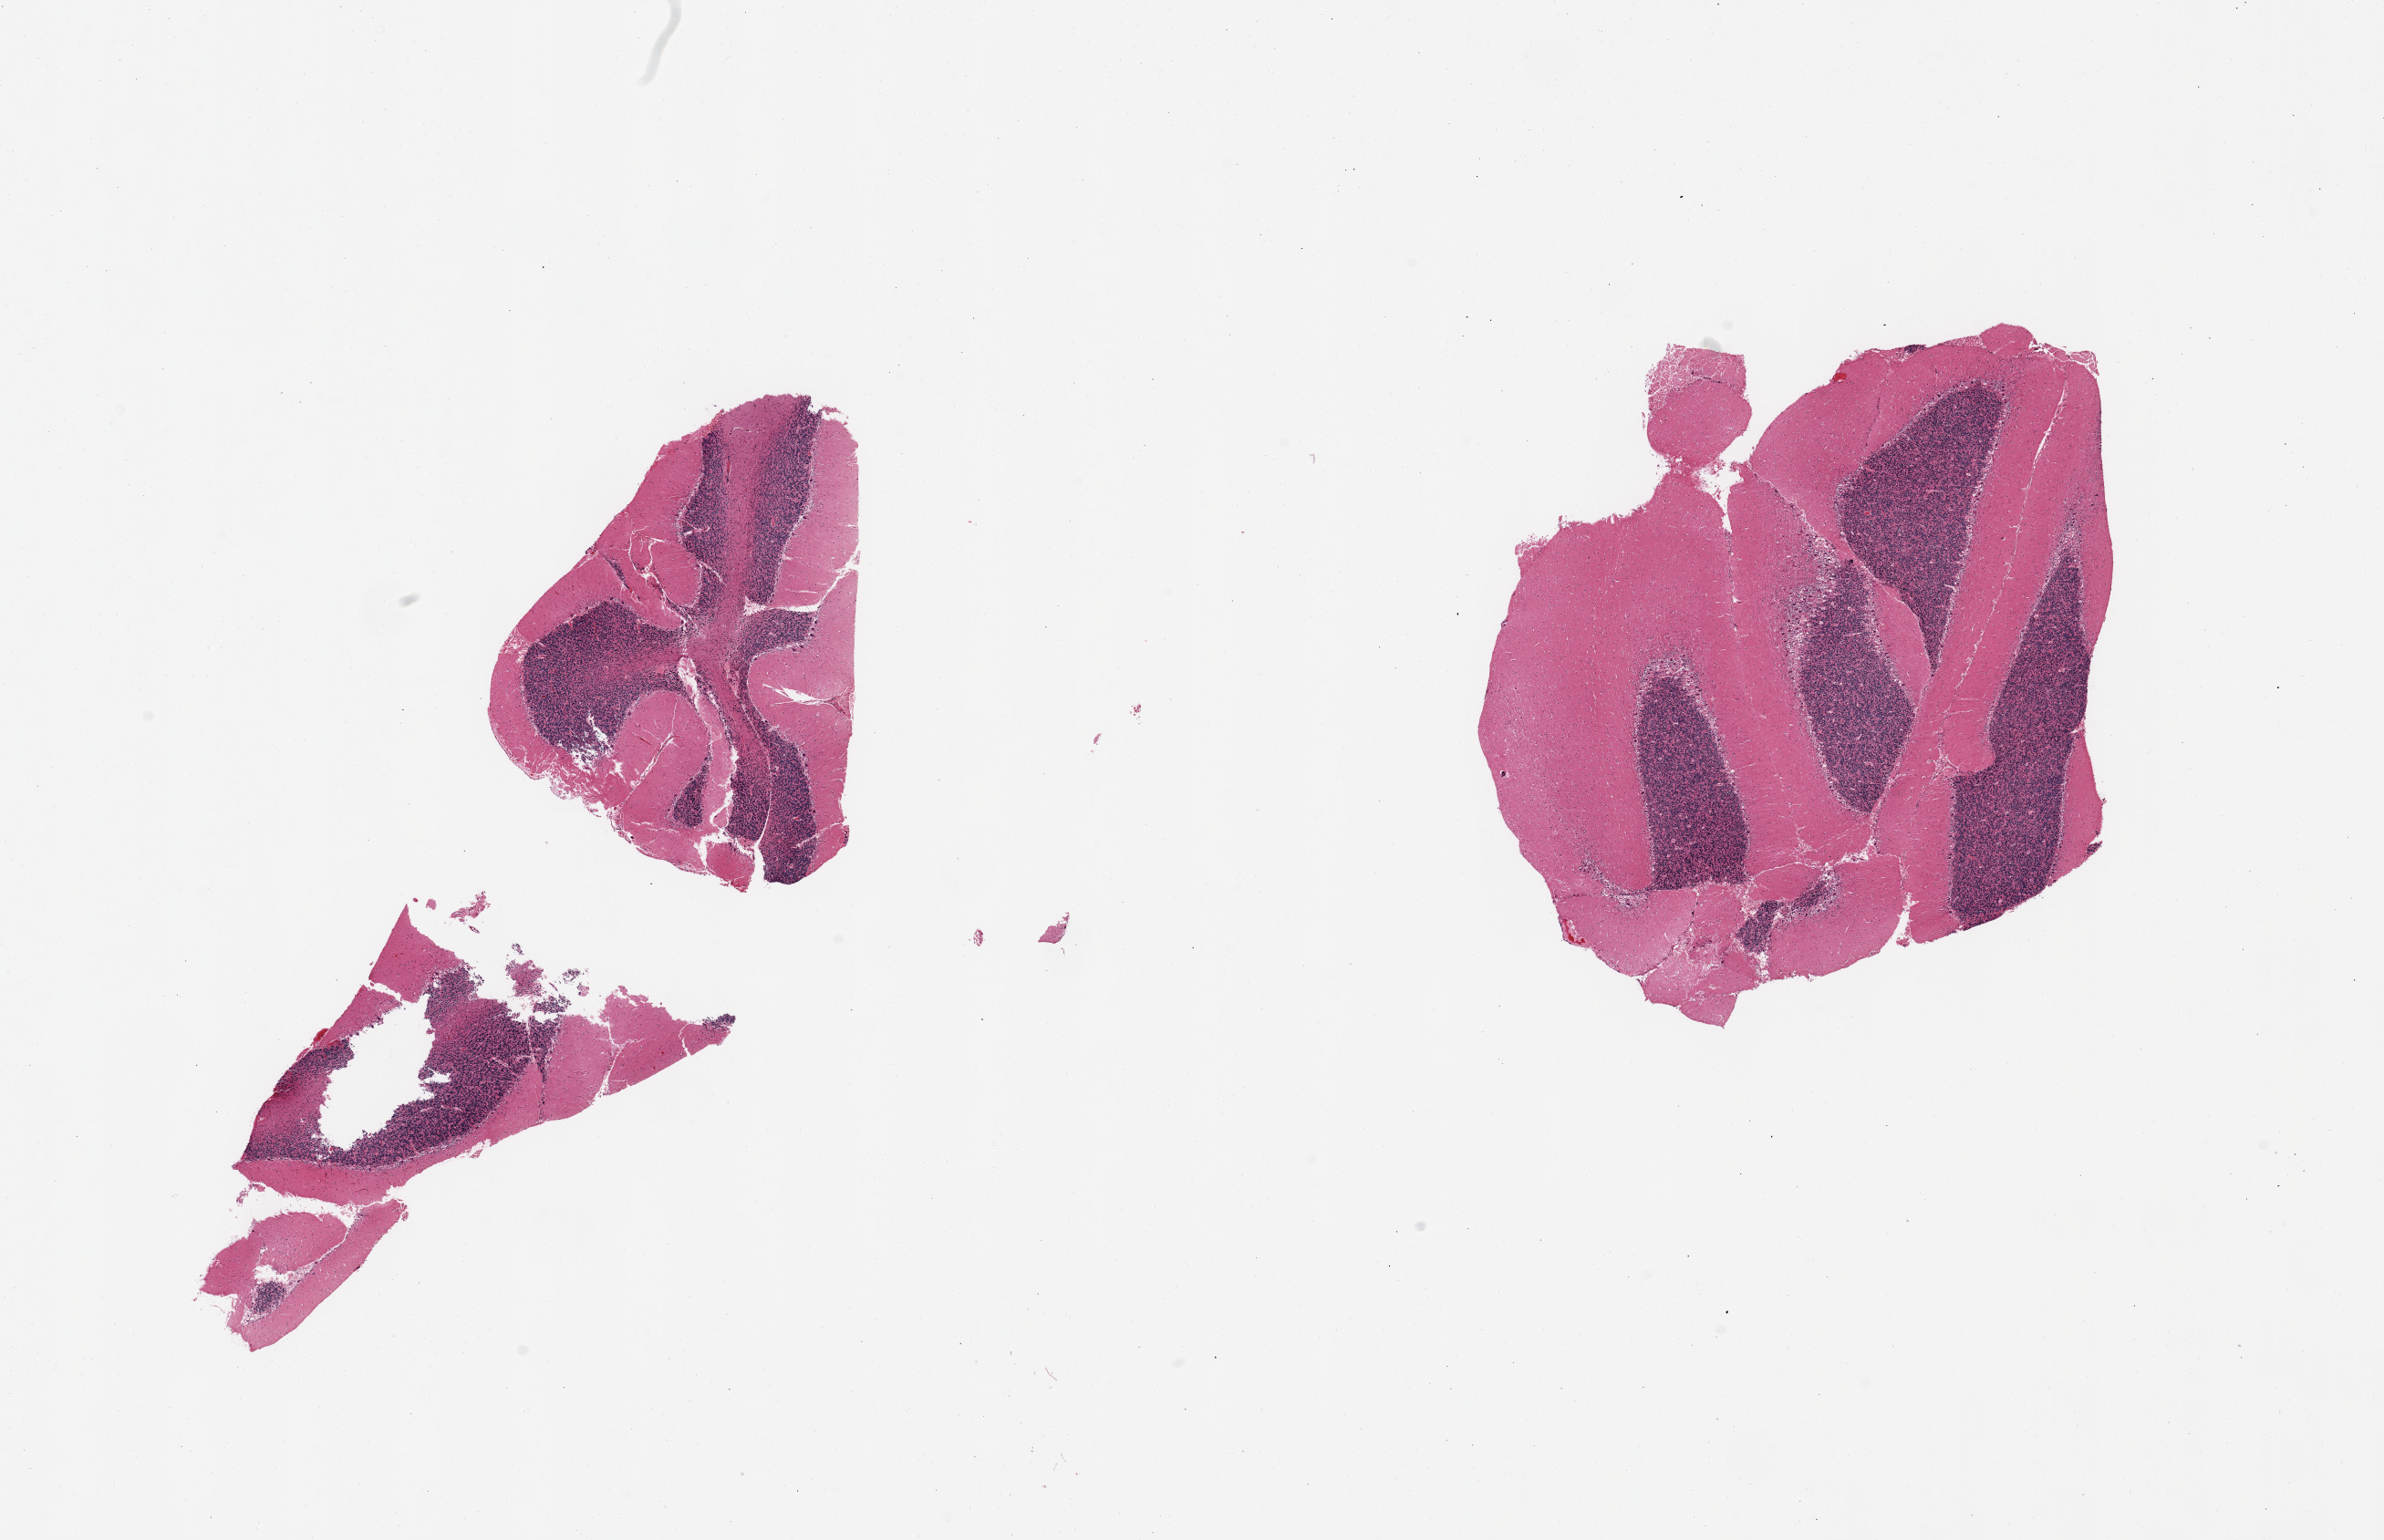
Haematoxylin and eosin whole-slide image — whole scanned area (about 20.7 x 13.4 mm, from a 20x scan) shown as a low-resolution overview; PAXgene-fixed paraffin-embedded (PFPE) section; target tissue: cerebellum; donor tissue sample. Donor sex: male.
- review note (as recorded): 2 pieces, no abnormalities